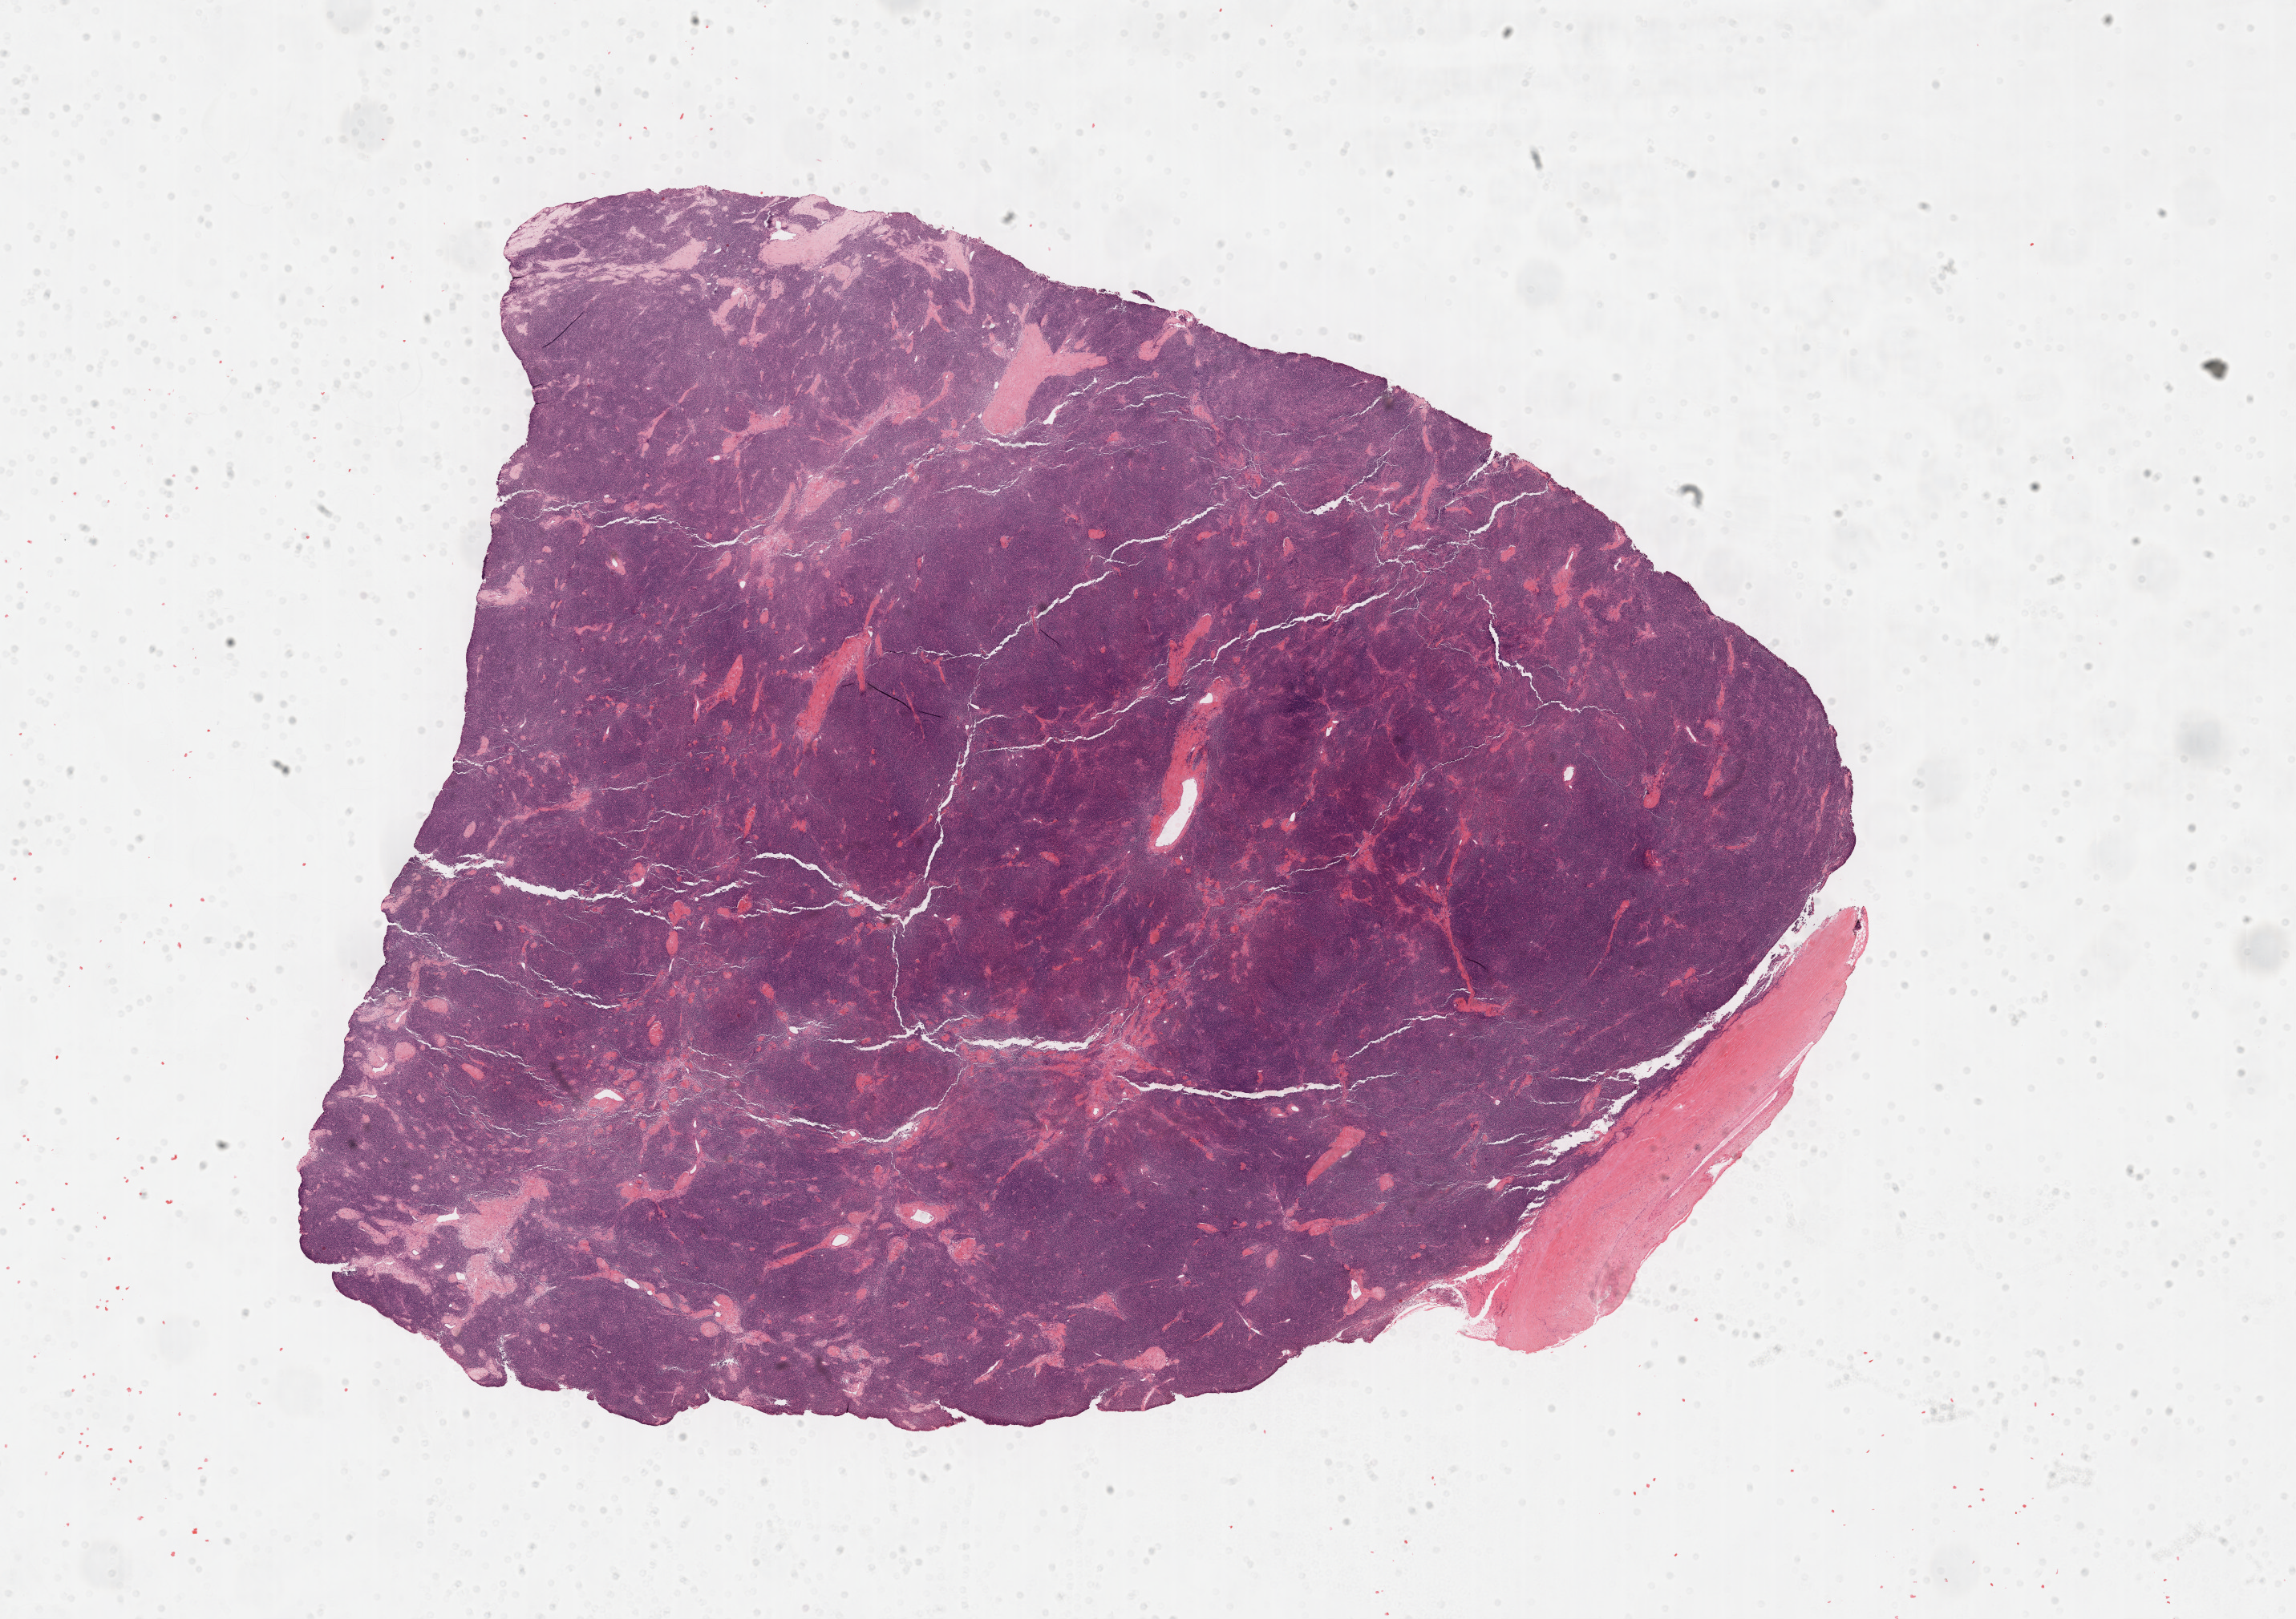
Digitized H&E tissue section (whole slide), a low-resolution overview of the entire scanned area, about 23.2 x 16.3 mm (from a 40x scan). Formalin-fixed paraffin-embedded (FFPE) diagnostic section. Sample: primary tumour, thymus. Male, age 45 years at initial diagnosis.
* histologic diagnosis: Thymoma, type B2, NOS